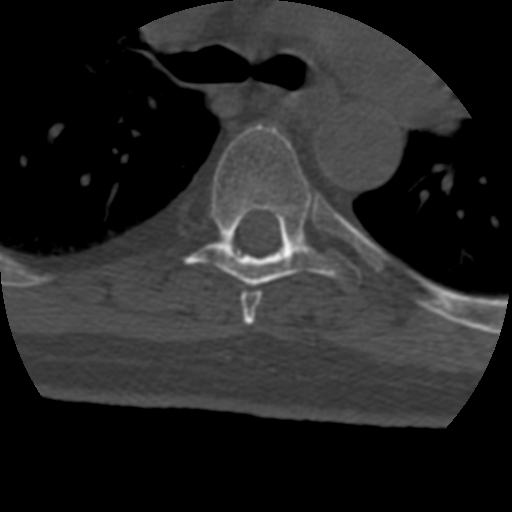
CT including the spine, one axial slice; position 302 of 399 along the scan axis; 120 kVp; bone window (W 1800 / L 400 HU); 512 × 512 image matrix, field of view 160 × 160 mm. Patient age 69 years. Case-level facts recorded for this patient, not image findings: primary cancer: prostate.
Structures marked on this image (semi-automatic segmentation, software-assisted and operator-edited):
- T5 vertebra: bounding box [x1, y1, x2, y2] px = [241, 291, 262, 326]
- T6 vertebra: [185, 125, 362, 289]